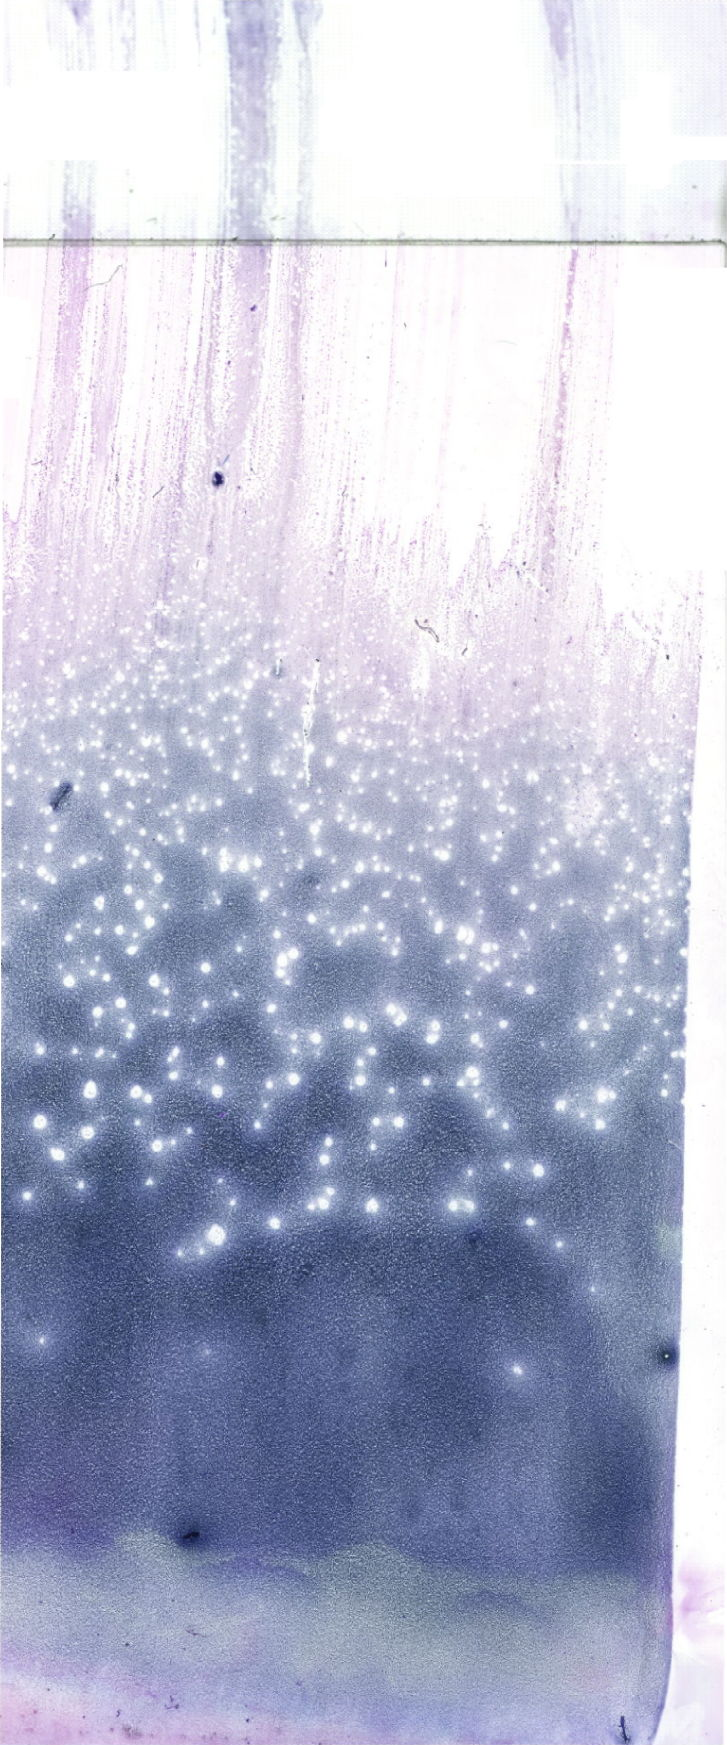
Bone marrow aspirate smear, May-Grünwald-Giemsa (MGG) stain, whole-slide image — whole scanned area (about 20.6 x 49.5 mm) shown as a low-resolution overview. Patient sex: female.
• diagnosis: B Acute Lymphoblastic Leukemia